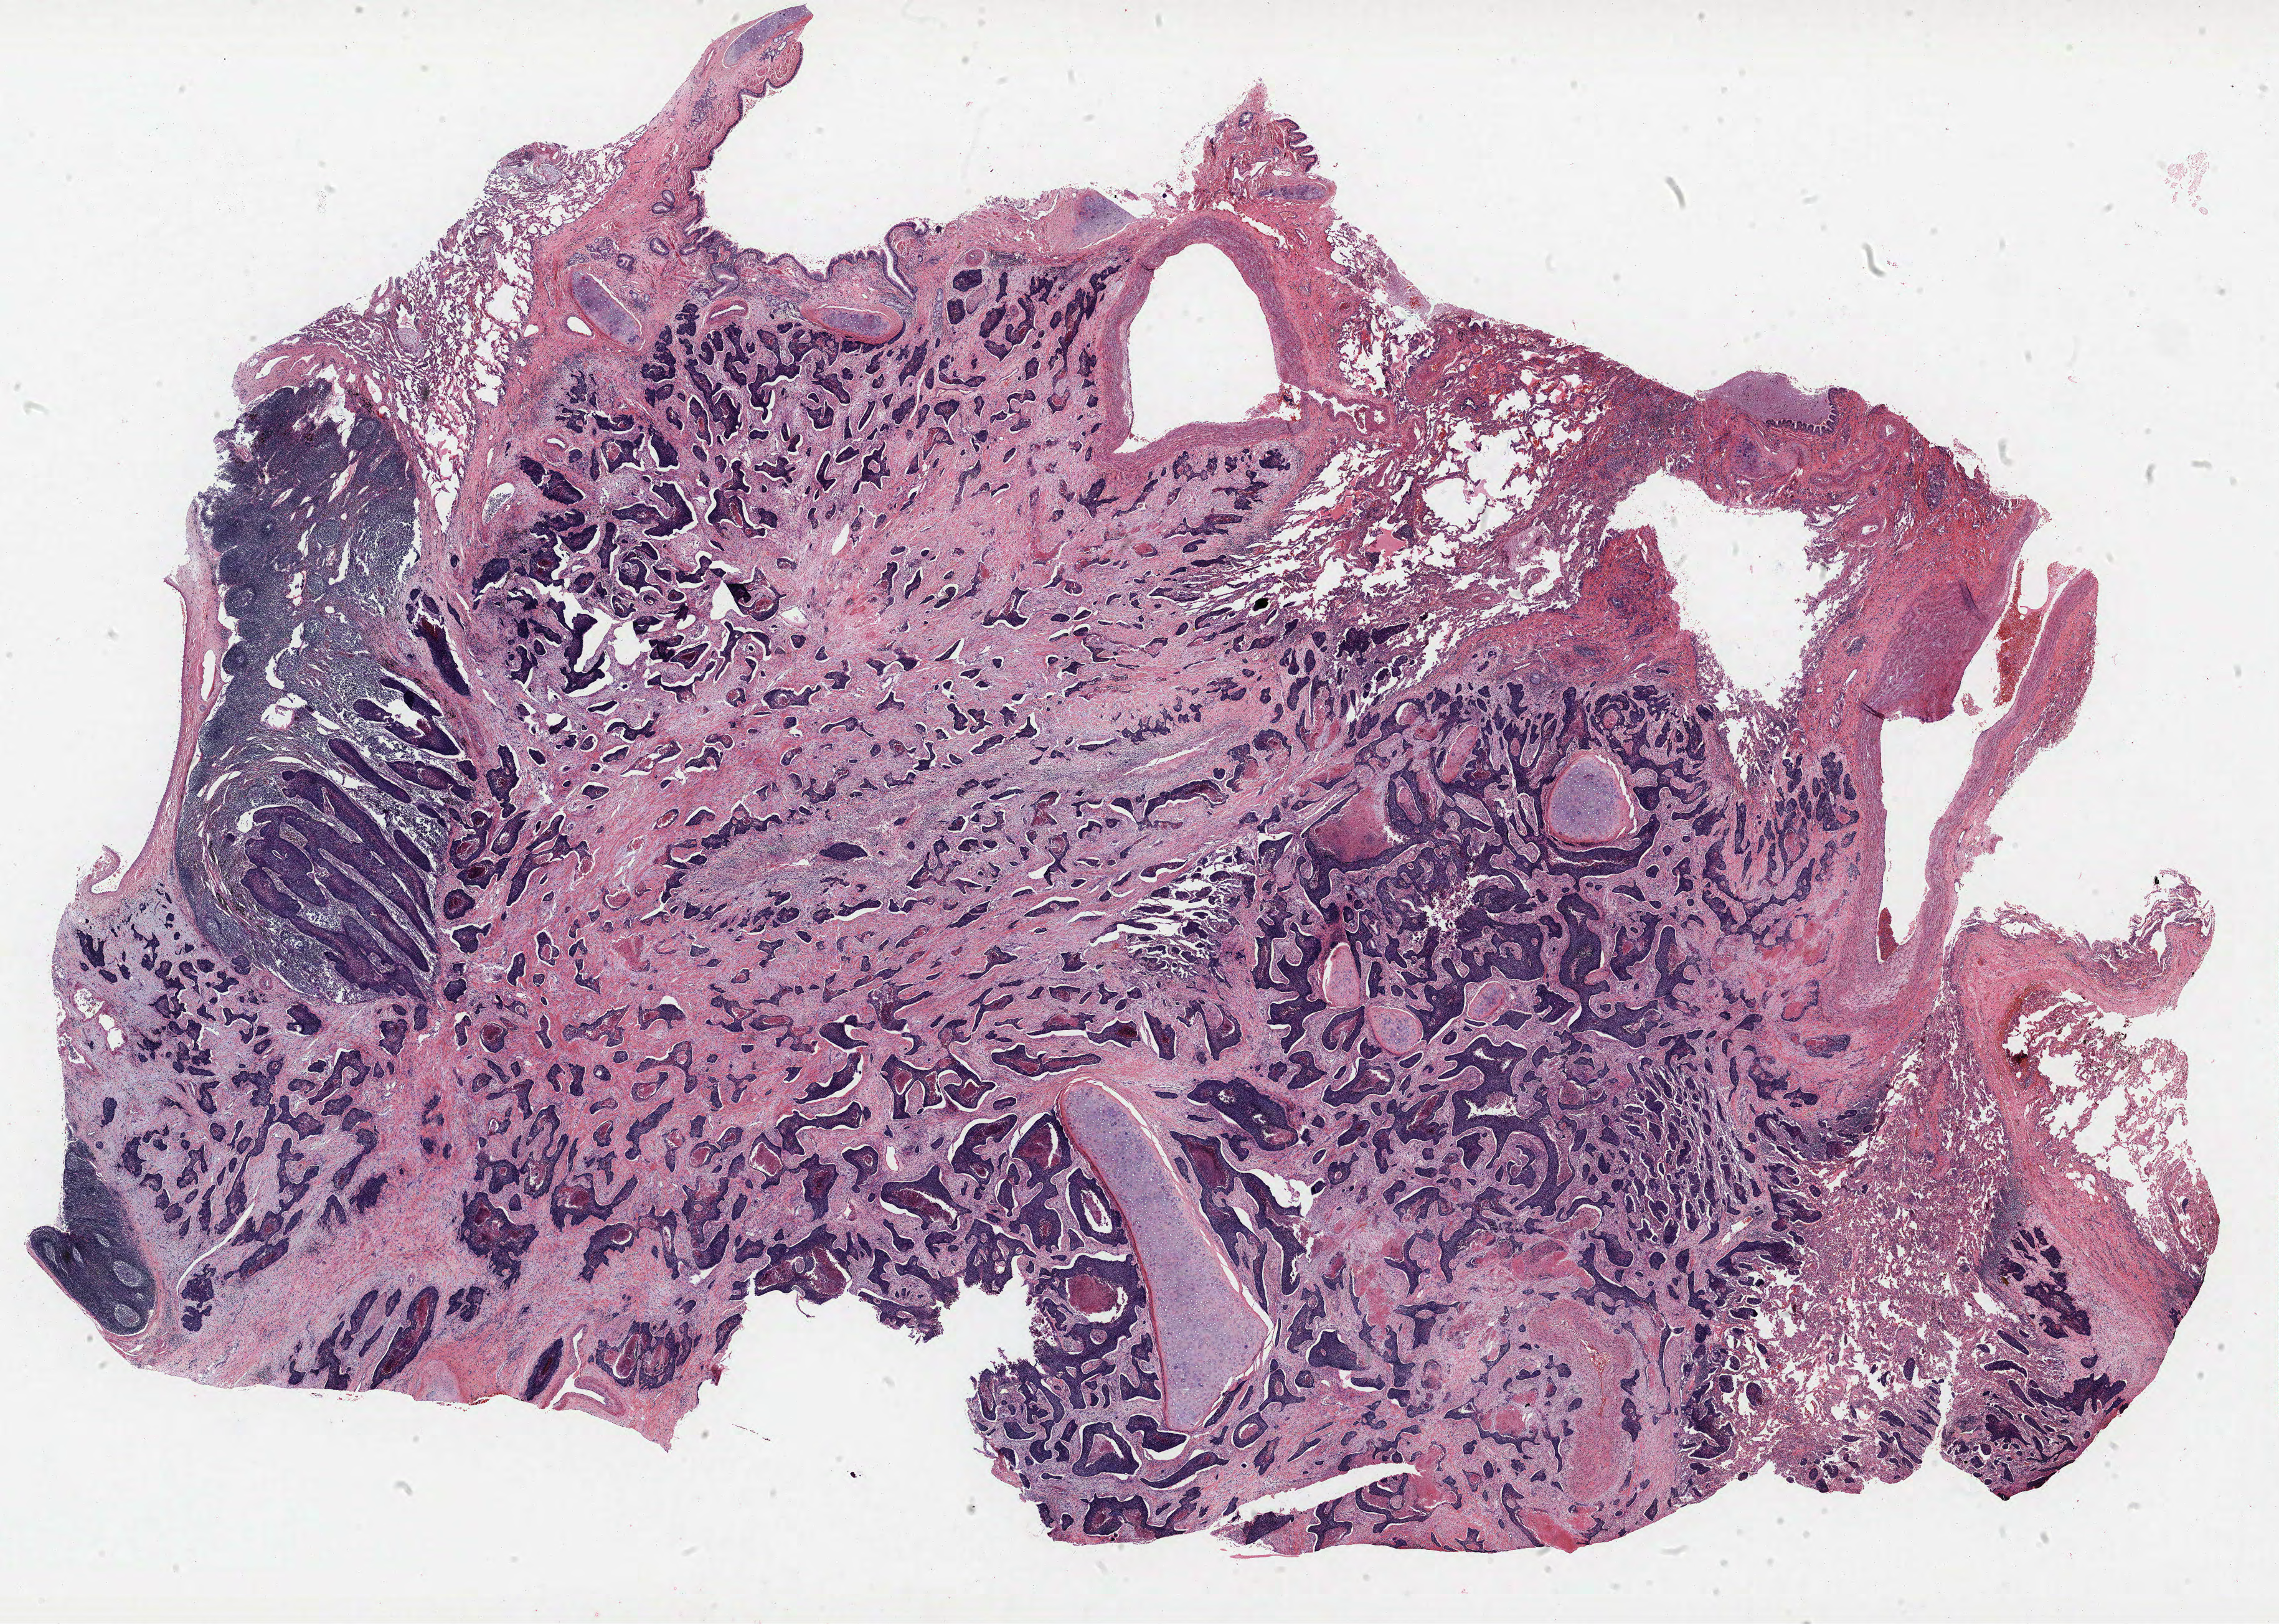
Whole-slide histology image, Hematoxylin and eosin (H&E) stained — low-resolution overview of the scanned area, about 29.3 x 20.9 mm (from a 40x scan). Formalin-fixed paraffin-embedded (FFPE) section. Lung. Female, age 57 at enrolment. Grade: moderately differentiated (G2).
* tumour size (pathology): 32 mm
* stage (AJCC 6th edition): IIB
* participant's lung-cancer diagnosis: Basaloid squamous cell carcinoma (ICD-O-3 8083/3)
* ICD-O-3 topography: lower lobe of lung (C34.3)
* primary tumour location (clinical record): left lower lobe